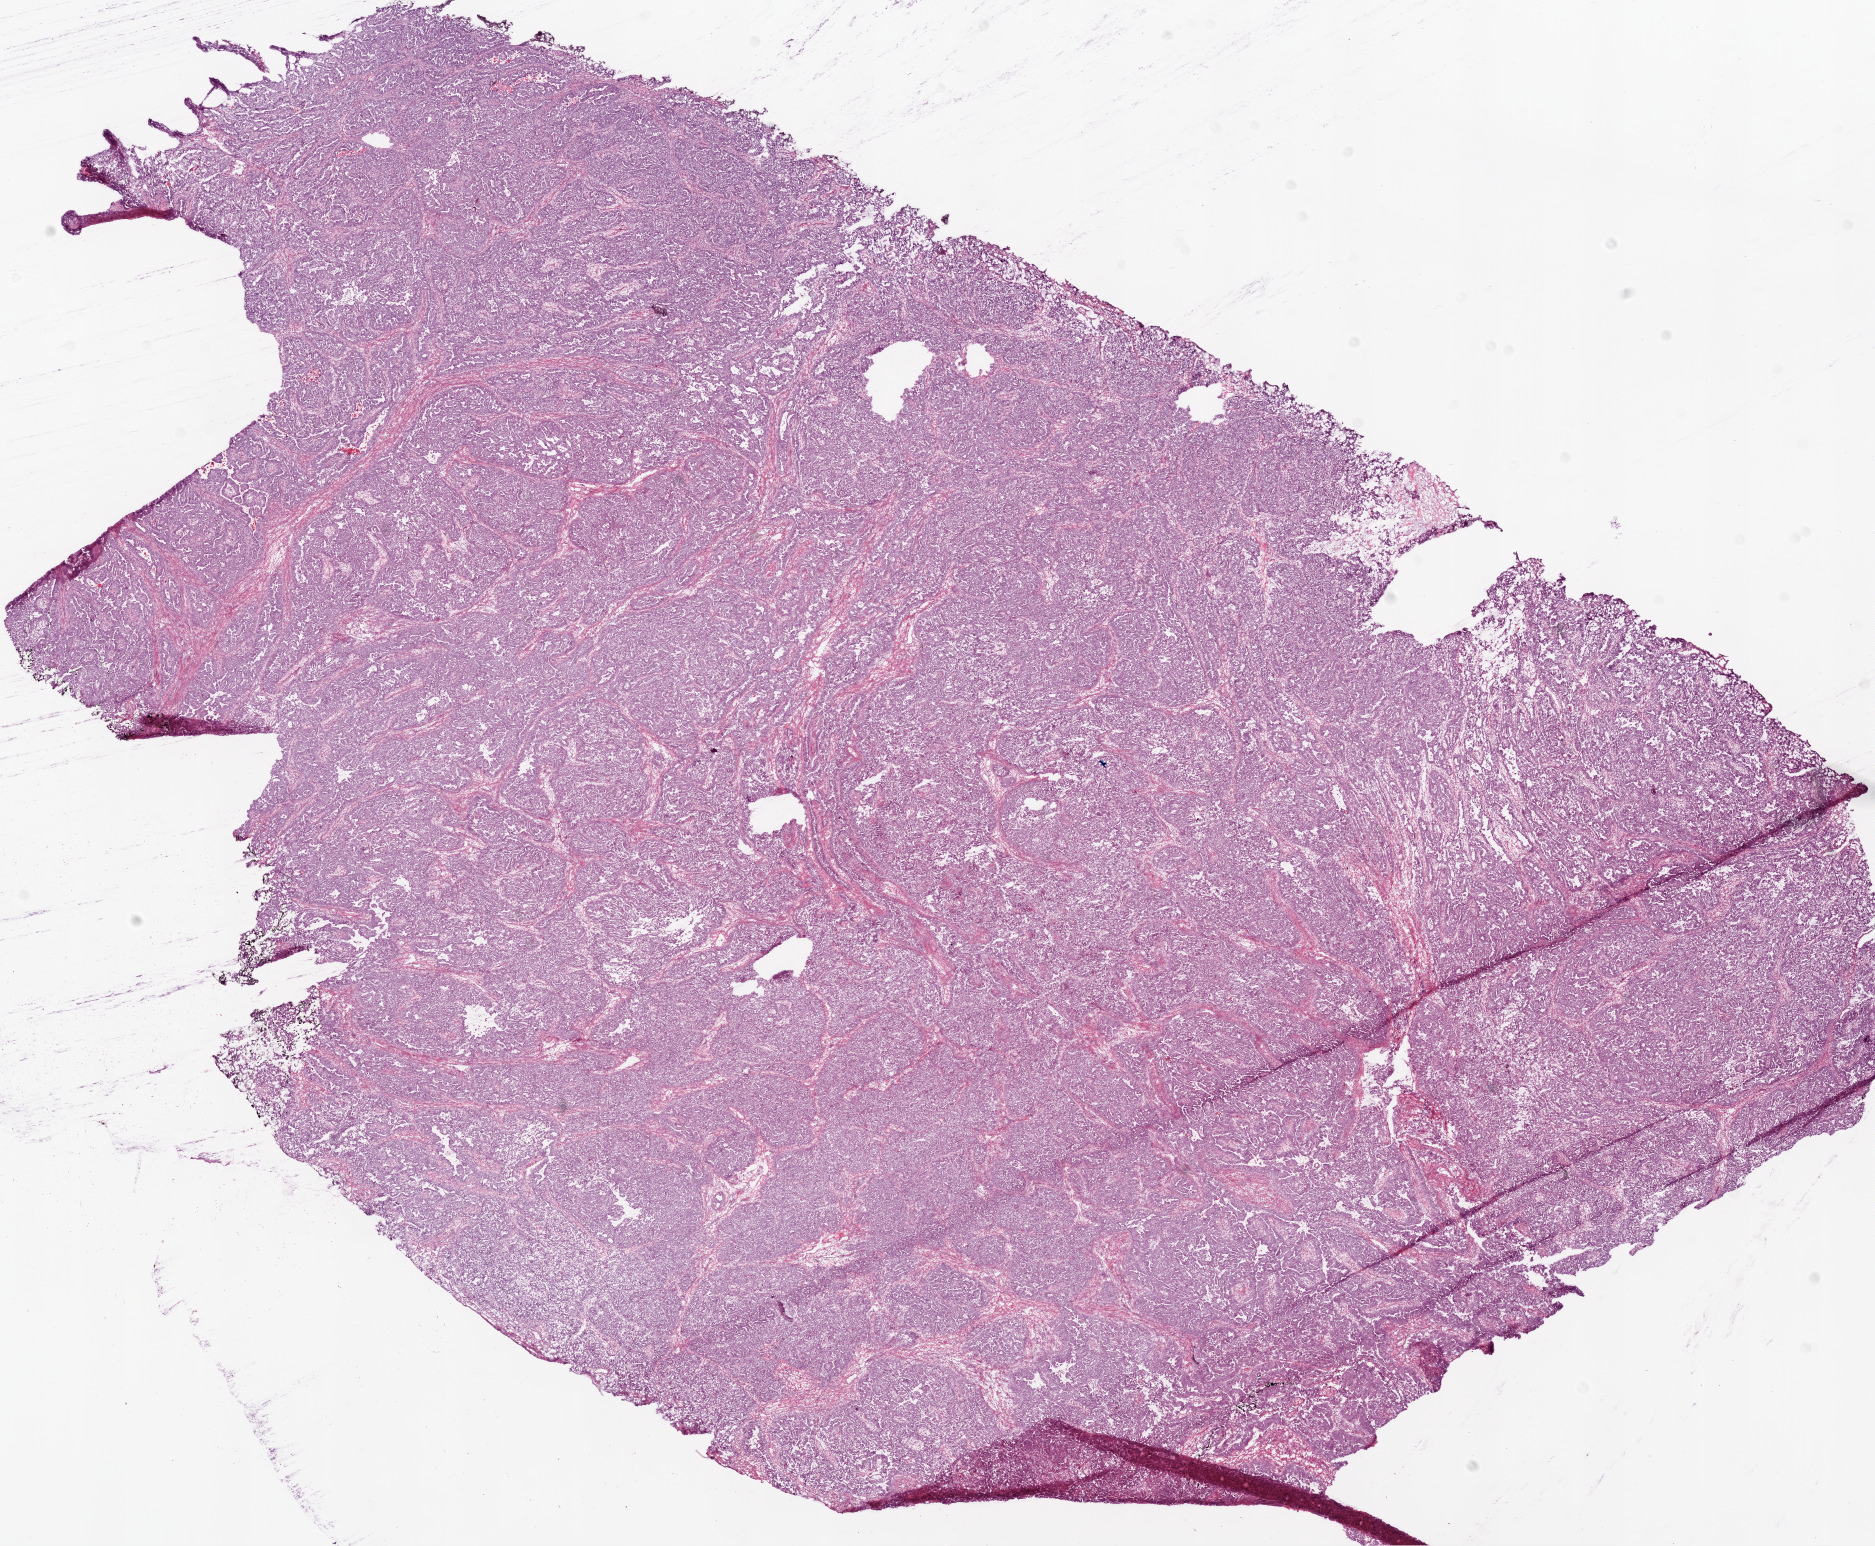
H&E-stained whole-slide image, whole scanned area (about 15.0 x 12.4 mm, from a 20x scan) shown as a low-resolution overview; frozen section; ovary, primary tumour sample. Female patient; age at initial diagnosis 66 years. Histologic grade: G3 (poorly differentiated). Pathologist review of this section (percent, as recorded): tumour cells 94%, tumour nuclei 95%, normal cells 0%, stromal cells 5%, necrosis 1%.
• laterality: bilateral
• pathologic diagnosis: Serous cystadenocarcinoma, NOS
• FIGO stage: IIIC